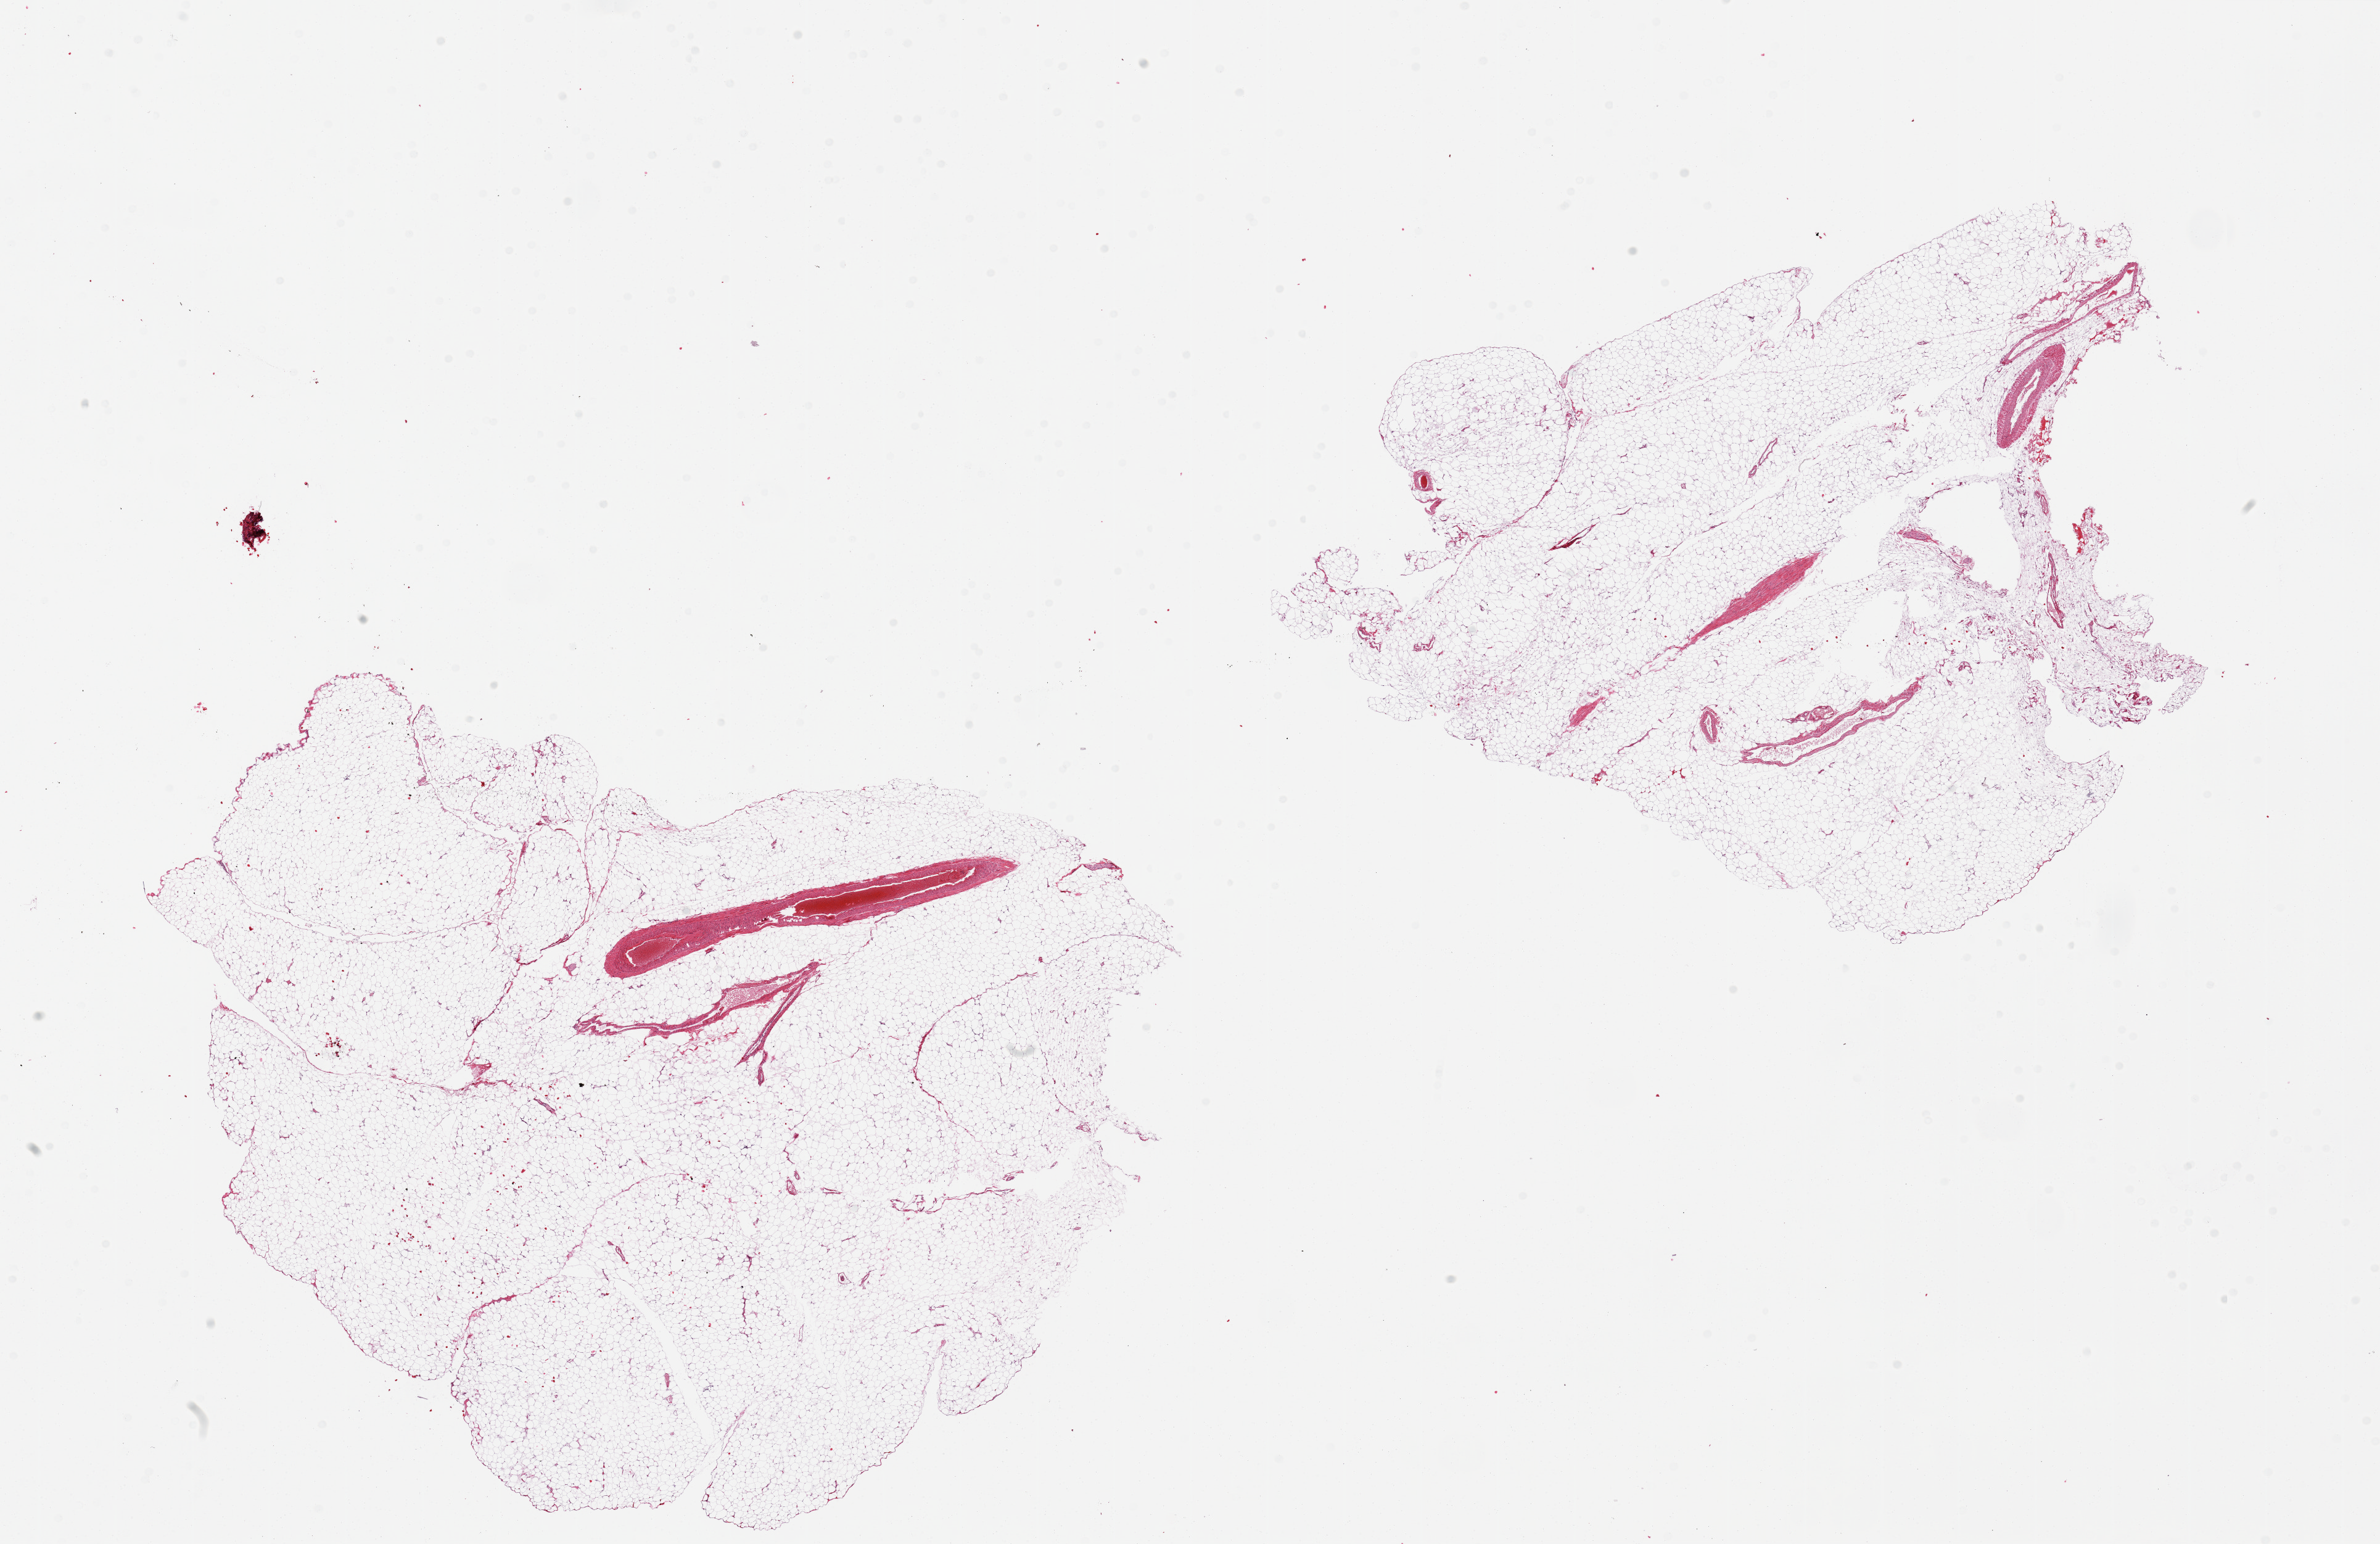
Digitized H&E-stained section, low-resolution overview of the scanned area, about 30.5 x 19.8 mm (acquisition: 20x scan); PAXgene-fixed paraffin-embedded (PFPE) section; sampled site (target tissue): omentum; tissue donor sample. Donor sex: male.
Review note (as recorded): 2 pieces, few large vessels.